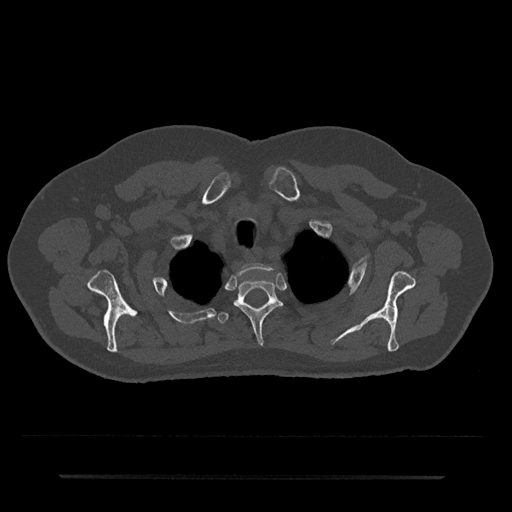
CT including the spine, one axial slice; slice 603 of 797 in the series (ordered by position); reconstruction kernel Br40s/3; bone window (W 1800 / L 400 HU); 0.5 mm slice thickness; 512 × 512 image matrix, field of view 437 × 437 mm. Male patient, age 69 years. Case-level facts recorded for this patient, not image findings: primary cancer: prostate.
Structures marked on this image (semi-automatically segmented with operator editing):
- T1 vertebra: box from (x=237, y=263) to (x=278, y=276) px
- T2 vertebra: (x=234, y=279)–(x=283, y=345)
- T3 vertebra: (x=217, y=312)–(x=229, y=324)